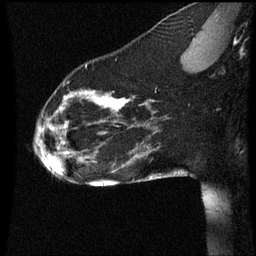
Breast MRI (dynamic contrast-enhanced), one sagittal slice. Slice 18 of 60 in the series (ordered by position). Dynamic contrast-enhanced series, image 2 of 3 at this slice position (ordered by acquisition). 1.5 T. TE 4.2 ms, TR 8.9 ms. 2 mm slice thickness. 256 × 256 image matrix, field of view 200 × 200 mm. Patient: female, 35 years. Case-level facts recorded for this patient, not image findings: setting: breast cancer imaged before/during neoadjuvant chemotherapy; receptor status: HER2-positive.
Annotated regions visible in this slice (semi-automatic segmentation, software-assisted and operator-edited):
- analysis volume of interest (the breast-tissue region the enhancement analysis was run in; not a lesion): bounding box [x1, y1, x2, y2] px = [33, 66, 177, 177]
- tumour enhancement mask (voxels above the 70 % enhancement threshold inside the analysis volume of interest): [49, 94, 148, 157]